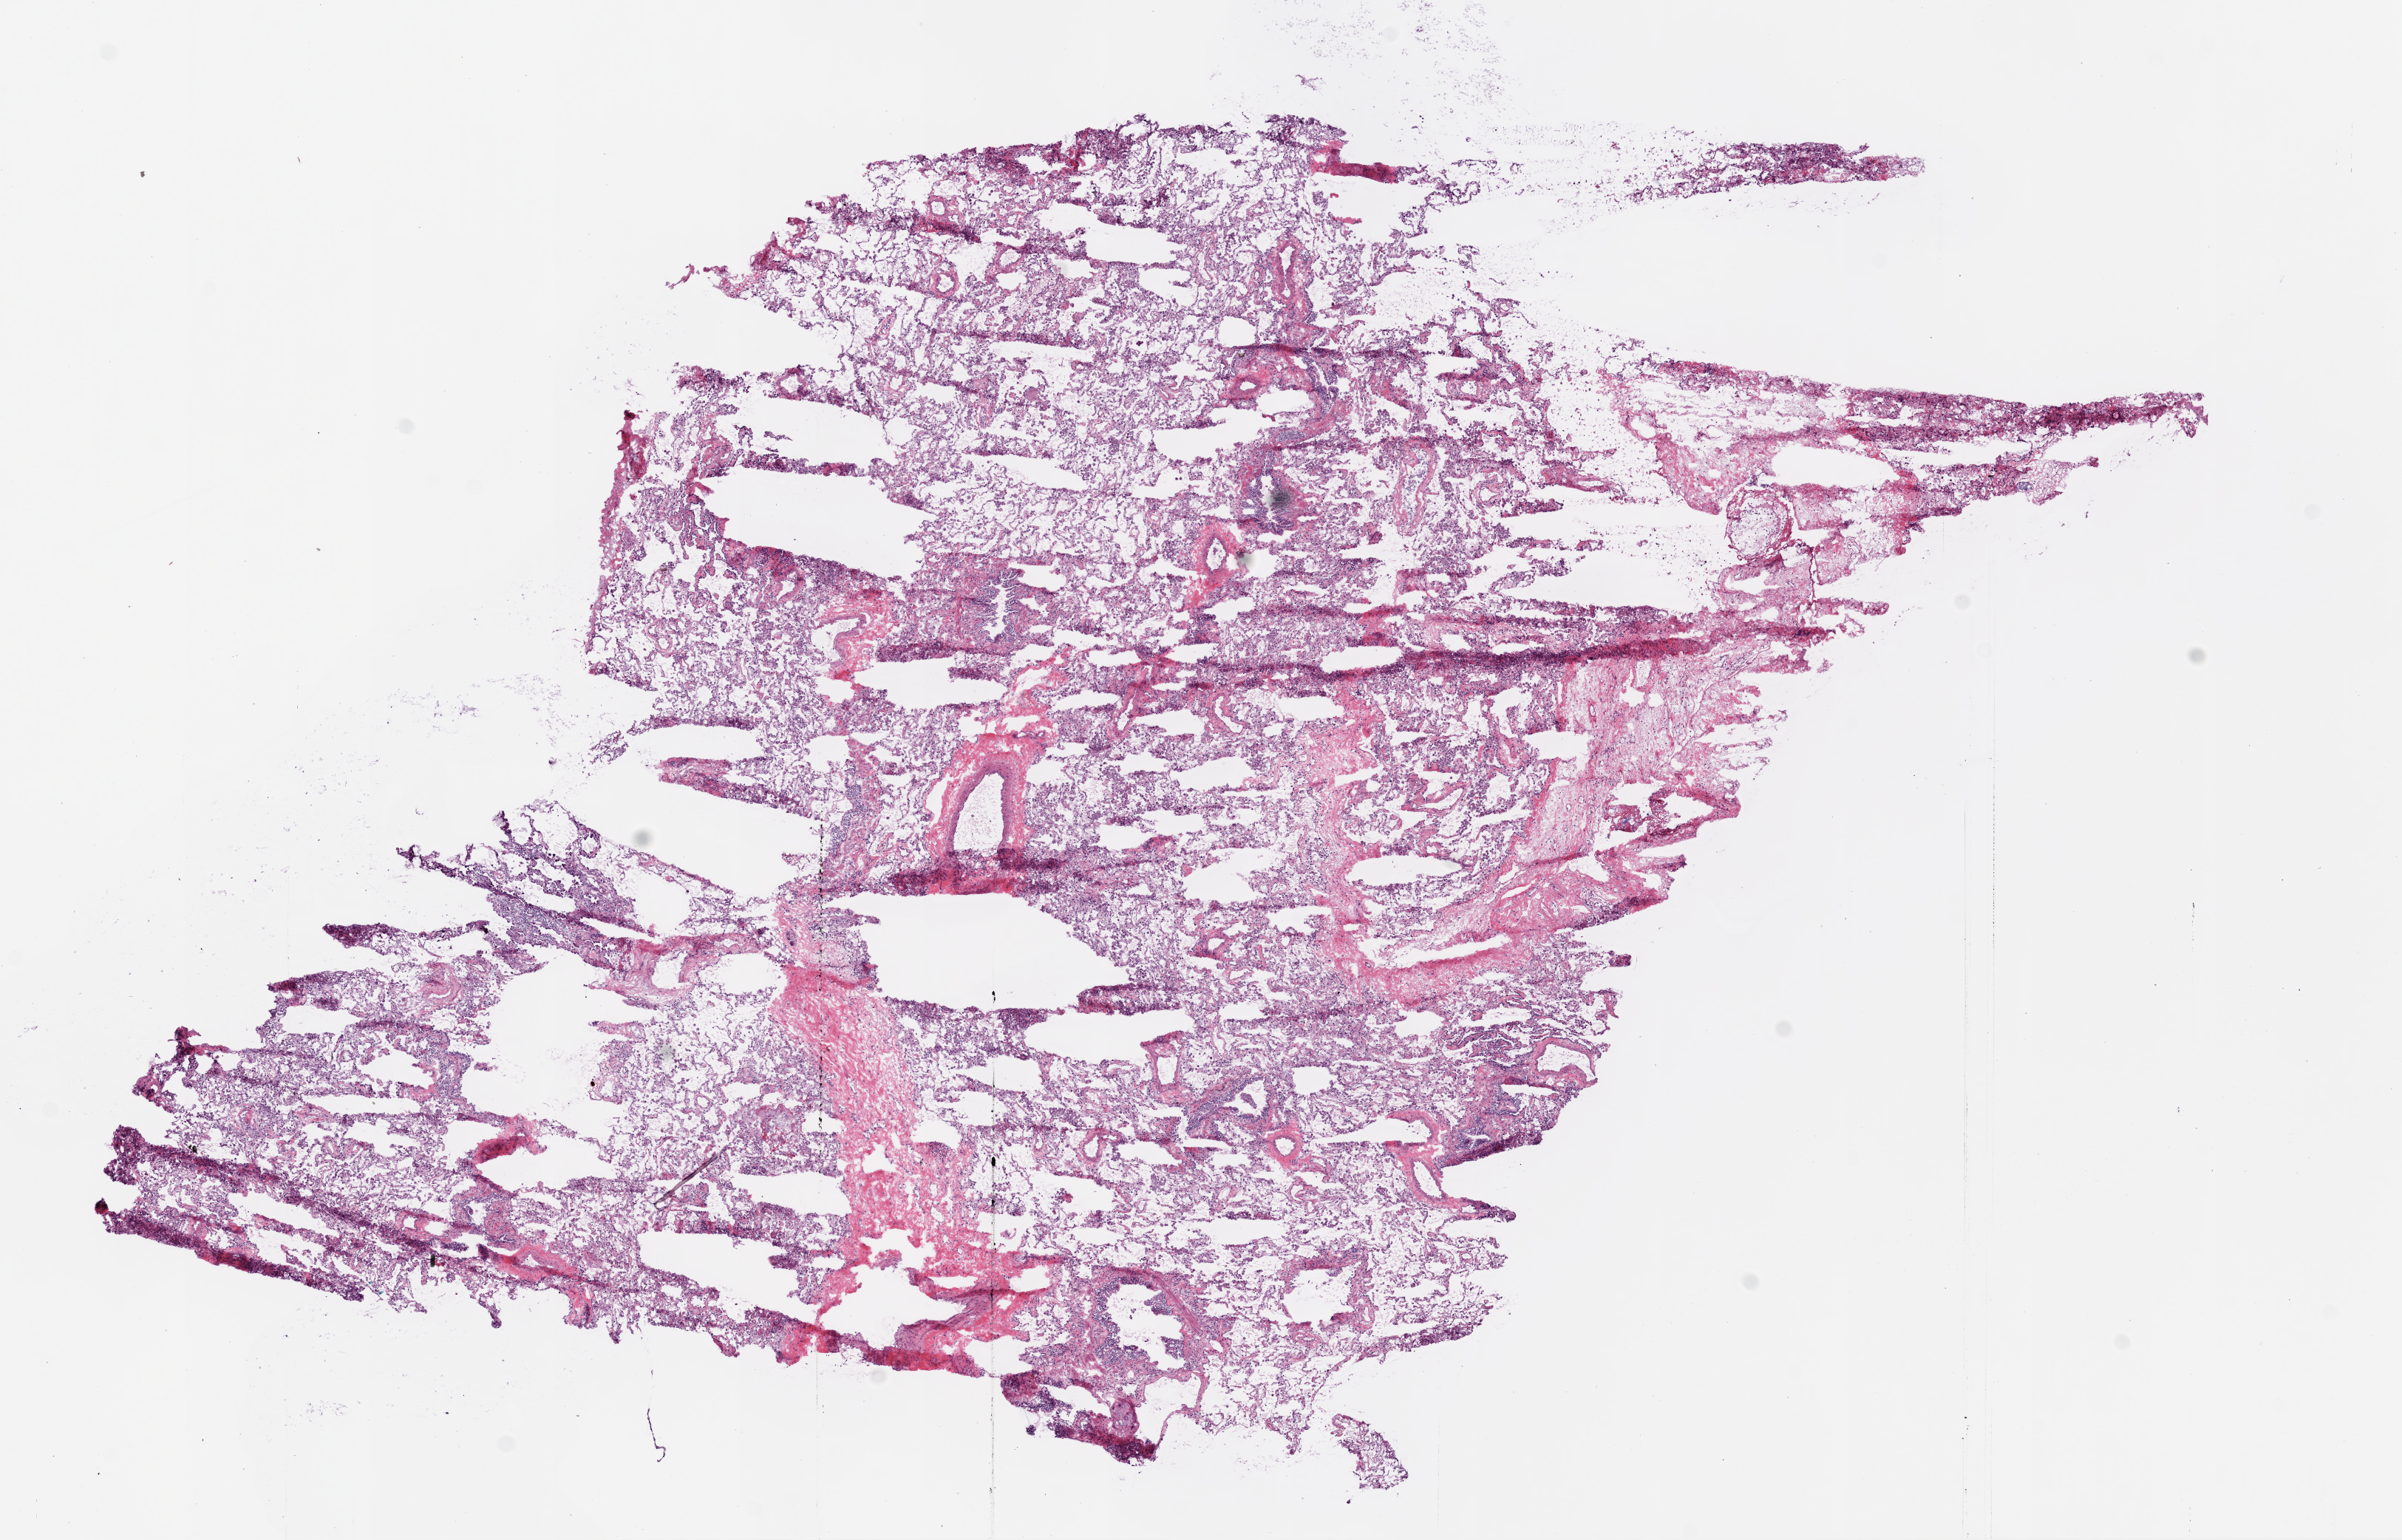
Whole-slide histology image, H&E — shown as a low-resolution overview of the whole scanned area (about 13.0 x 8.4 mm, from a 20x scan), frozen section from the bottom of the tissue portion, sample: solid tissue normal (non-tumour tissue), lung. Male, age 69 years at initial diagnosis.
This section: solid tissue normal sample (biorepository sample class). Patient diagnosis: Squamous cell carcinoma, NOS.